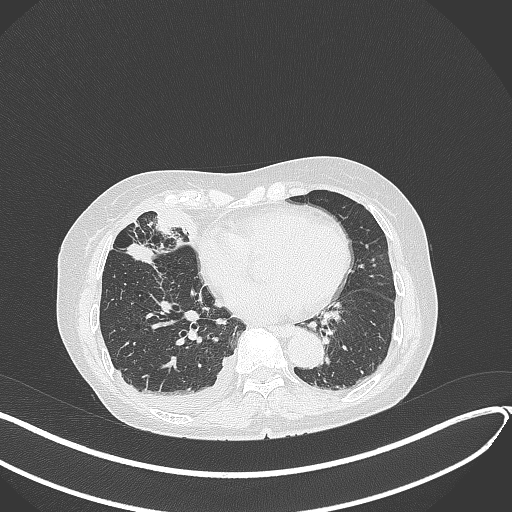
Chest CT, one axial slice; slice 149 of 418 in the series (ordered by position); 120 kVp; lung window (W 1500 / L -600 HU); 1 mm slice thickness; 512 × 512 image matrix. Patient: female, 75 years. Case-level facts recorded for this patient, not image findings: clinical TNM (as recorded): T2a N3 M0.
Annotated regions visible in this slice (bounding box drawn by a radiologist):
- lung tumour (recorded histology: adenocarcinoma): bounding box <124,240,161,269> (left, top, right, bottom; pixels)